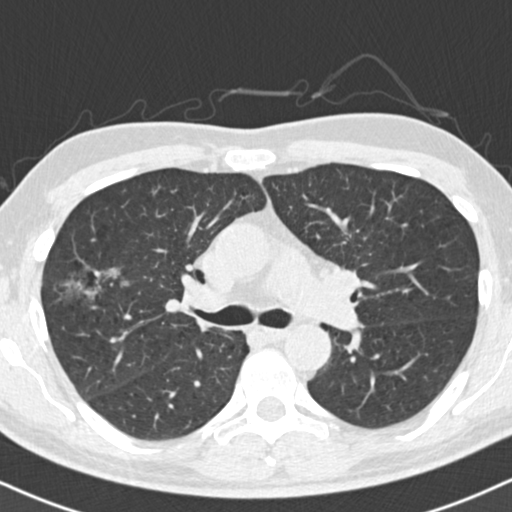
Axial slice from a low-dose chest CT screening exam; baseline annual screen; lung window (W 1500 / L -600 HU); 2 mm slice thickness; slice 60 of 154 in the series; 512 × 512 image matrix. Male, age 56 years at enrolment.
Expert-annotated lung lesion, bounding box [x1, y1, x2, y2] px = [51, 254, 140, 318]. No non-calcified nodule or mass ≥4 mm was recorded by the screening reader at this exam. Lung cancer was diagnosed 392 days after this screen: bronchiolo-alveolar adenocarcinoma, NOS, right upper lobe, well differentiated (G1), stage IIB (AJCC 6th edition), 30 mm at pathology.